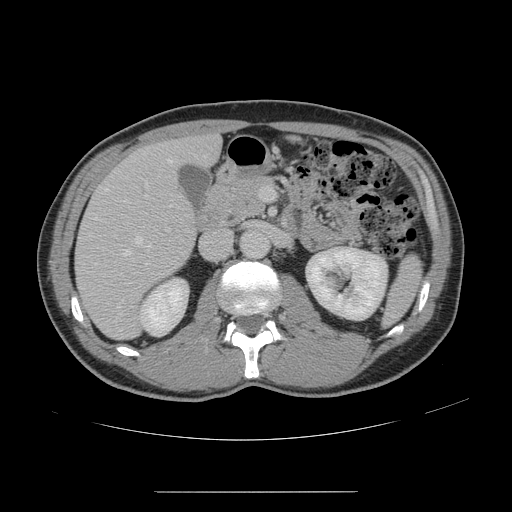
Contrast-enhanced abdominal CT, one axial slice. Slice 73 of 178 in the series (ordered by position). Intravenous contrast given. Soft-tissue window (W 400 / L 40 HU). 2.5 mm slice thickness. 512 × 512 image matrix, field of view 401 × 401 mm. Male patient, age 53 years. Case-level facts recorded for this patient, not image findings: diagnosis: colorectal cancer liver metastases, imaged before liver resection; multiple liver metastases: yes; largest metastasis: 2.4 cm; chemotherapy before resection: yes.
Annotated regions visible in this slice (expert manual segmentation):
- hepatic veins: box from (x=95, y=160) to (x=172, y=308) px
- liver: (x=76, y=137)–(x=221, y=340)
- planned liver remnant (the part of the liver to remain after resection): (x=185, y=137)–(x=220, y=162)
- portal vein (with intrahepatic branches): (x=145, y=187)–(x=267, y=201)